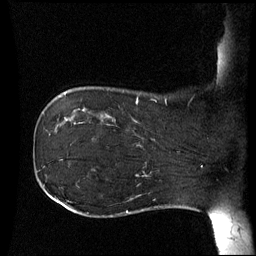
Breast MRI (dynamic contrast-enhanced), one sagittal slice; position 13 of 60 along the scan axis; dynamic contrast-enhanced series, image 2 of 3 at this slice position (ordered by acquisition); 1.5 T; TE 4.2 ms, TR 8.9 ms; 256 × 256 image matrix, field of view 230 × 230 mm. Patient: female, 42 years. From the clinical record (not read from this slice): setting: breast cancer imaged before/during neoadjuvant chemotherapy; receptor status: HER2-positive.
Structures marked on this image (semi-automatically segmented with operator editing):
- analysis volume of interest (the breast-tissue region the enhancement analysis was run in; not a lesion): bounding box [x1, y1, x2, y2] px = [106, 102, 173, 150]
- tumour enhancement mask (voxels above the 70 % enhancement threshold inside the analysis volume of interest): [136, 102, 140, 146]